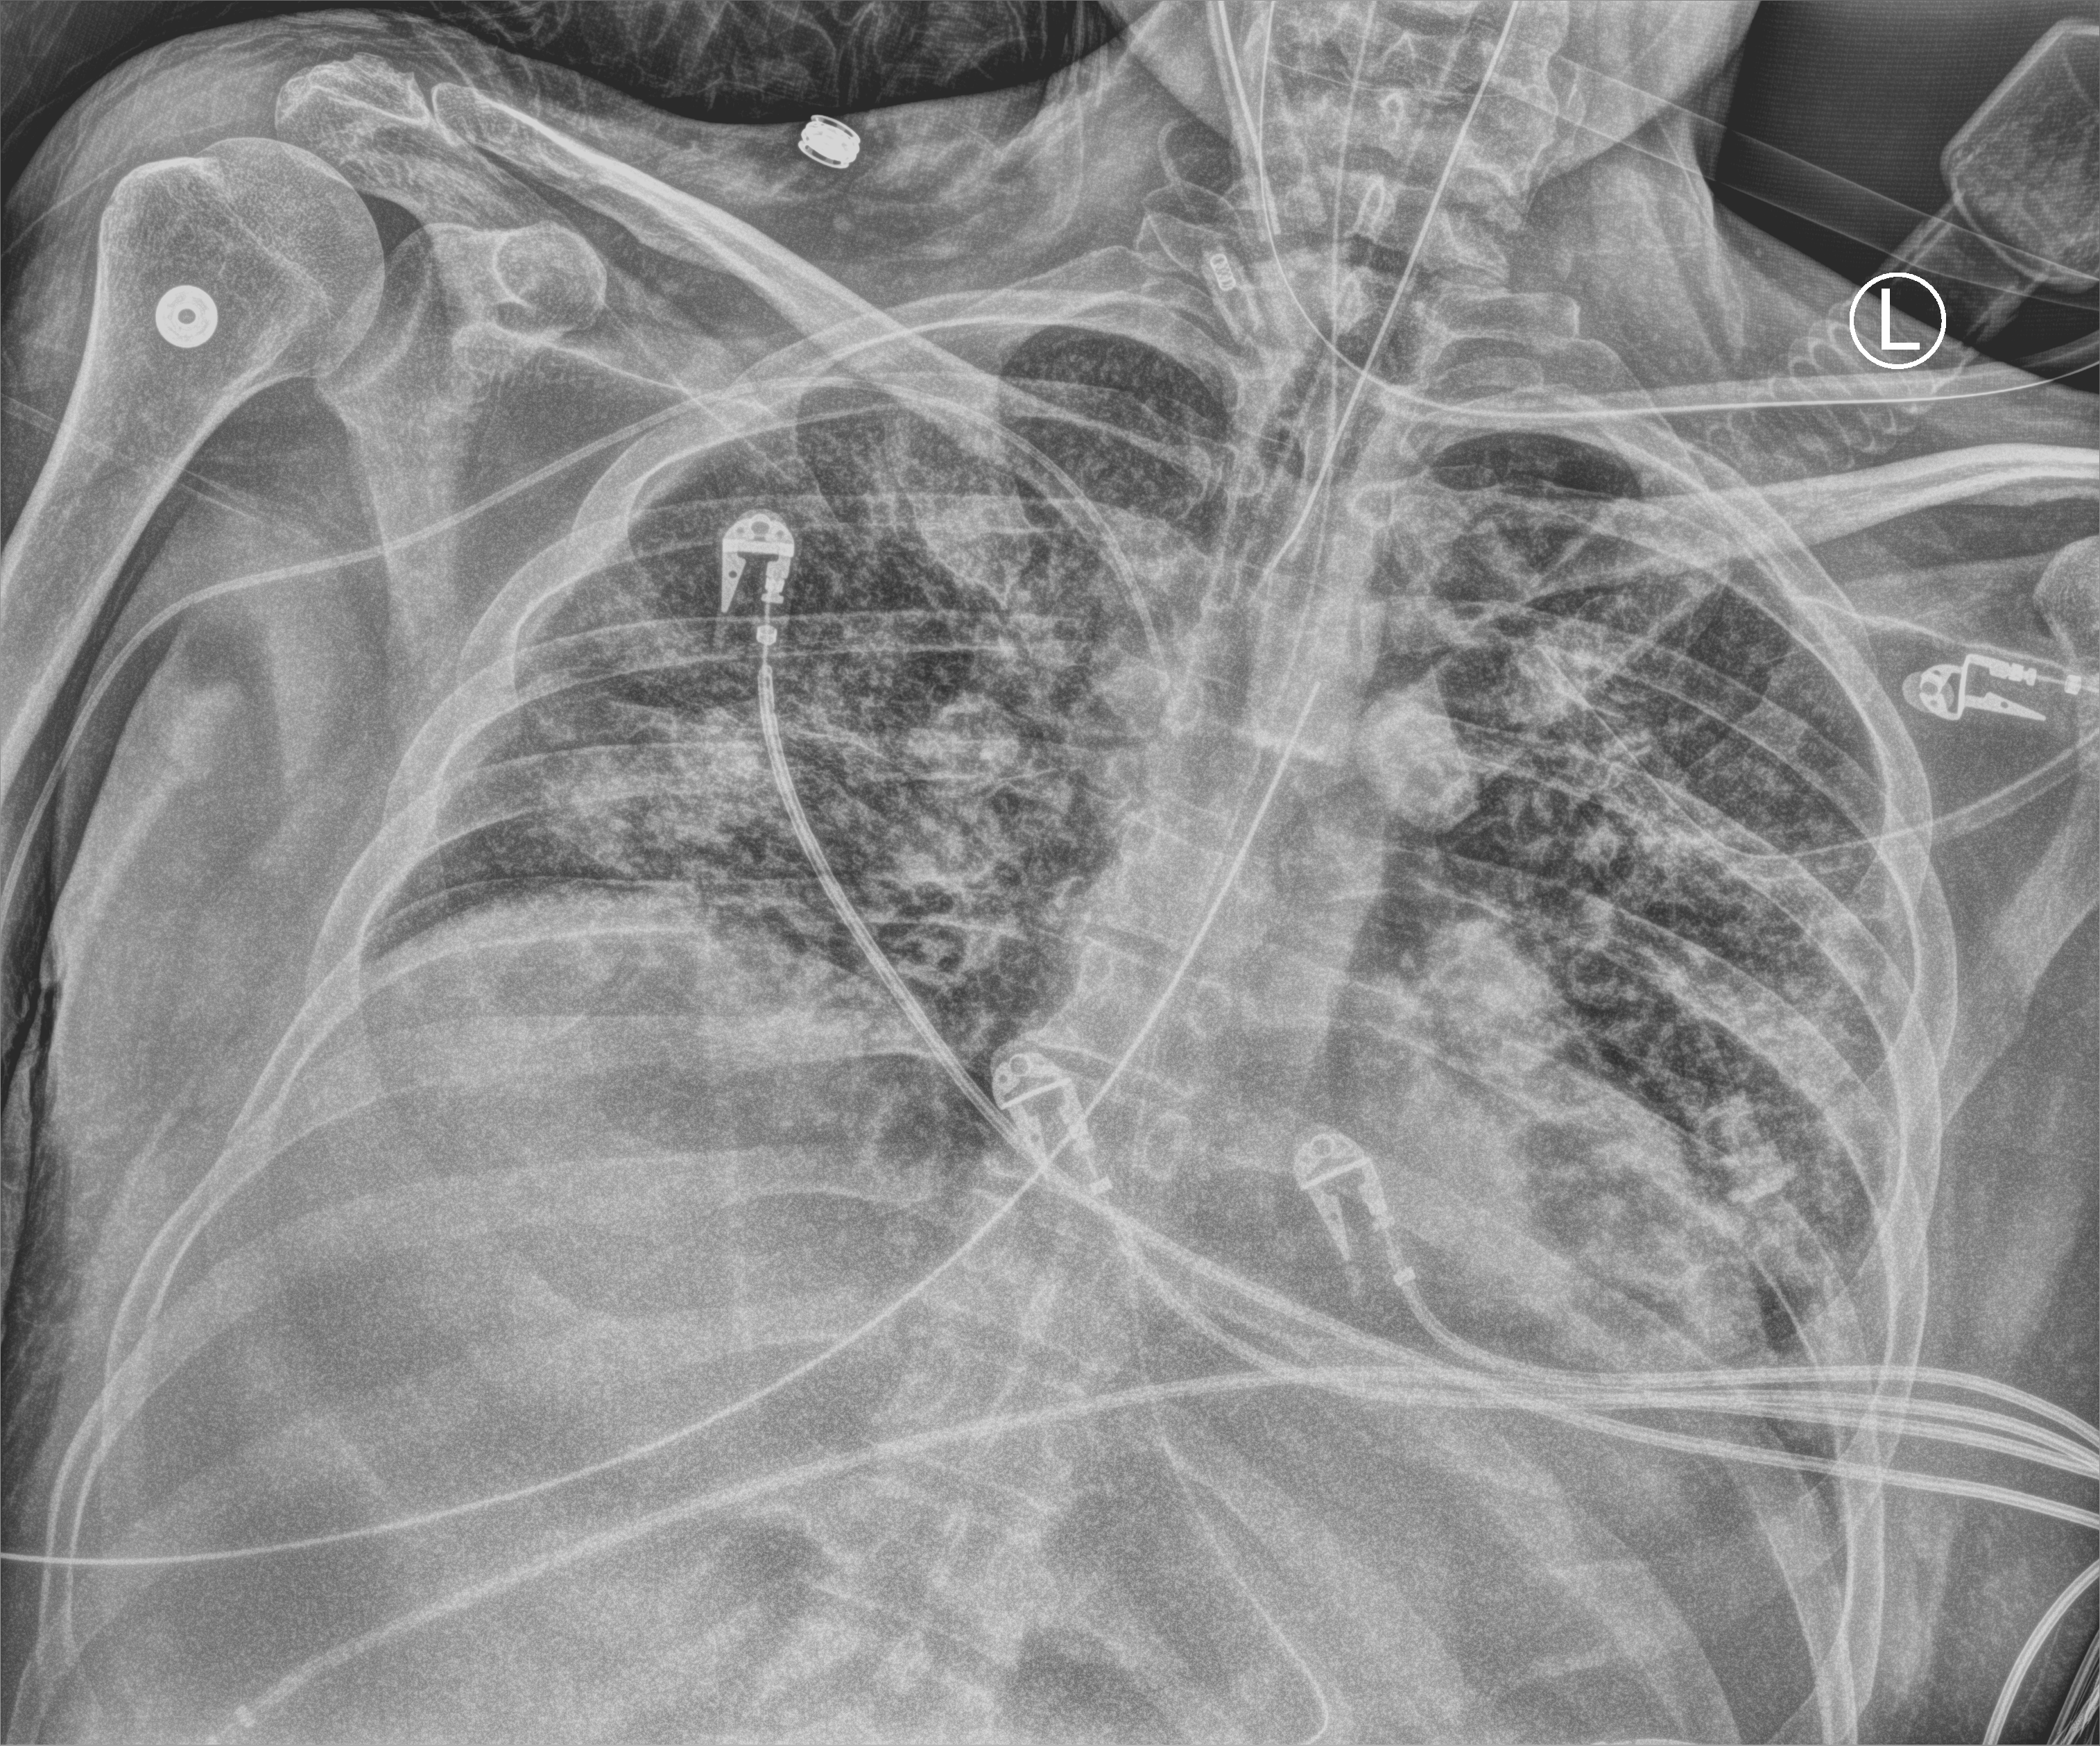
Portable chest radiograph; anteroposterior (AP) projection. Male patient hospitalised with COVID-19, age 18–59 years.
From the hospital-stay record, not from the radiograph (when in the stay this image was taken is not recorded): mechanically ventilated during this hospital stay: yes; length of hospital stay: 48 days.